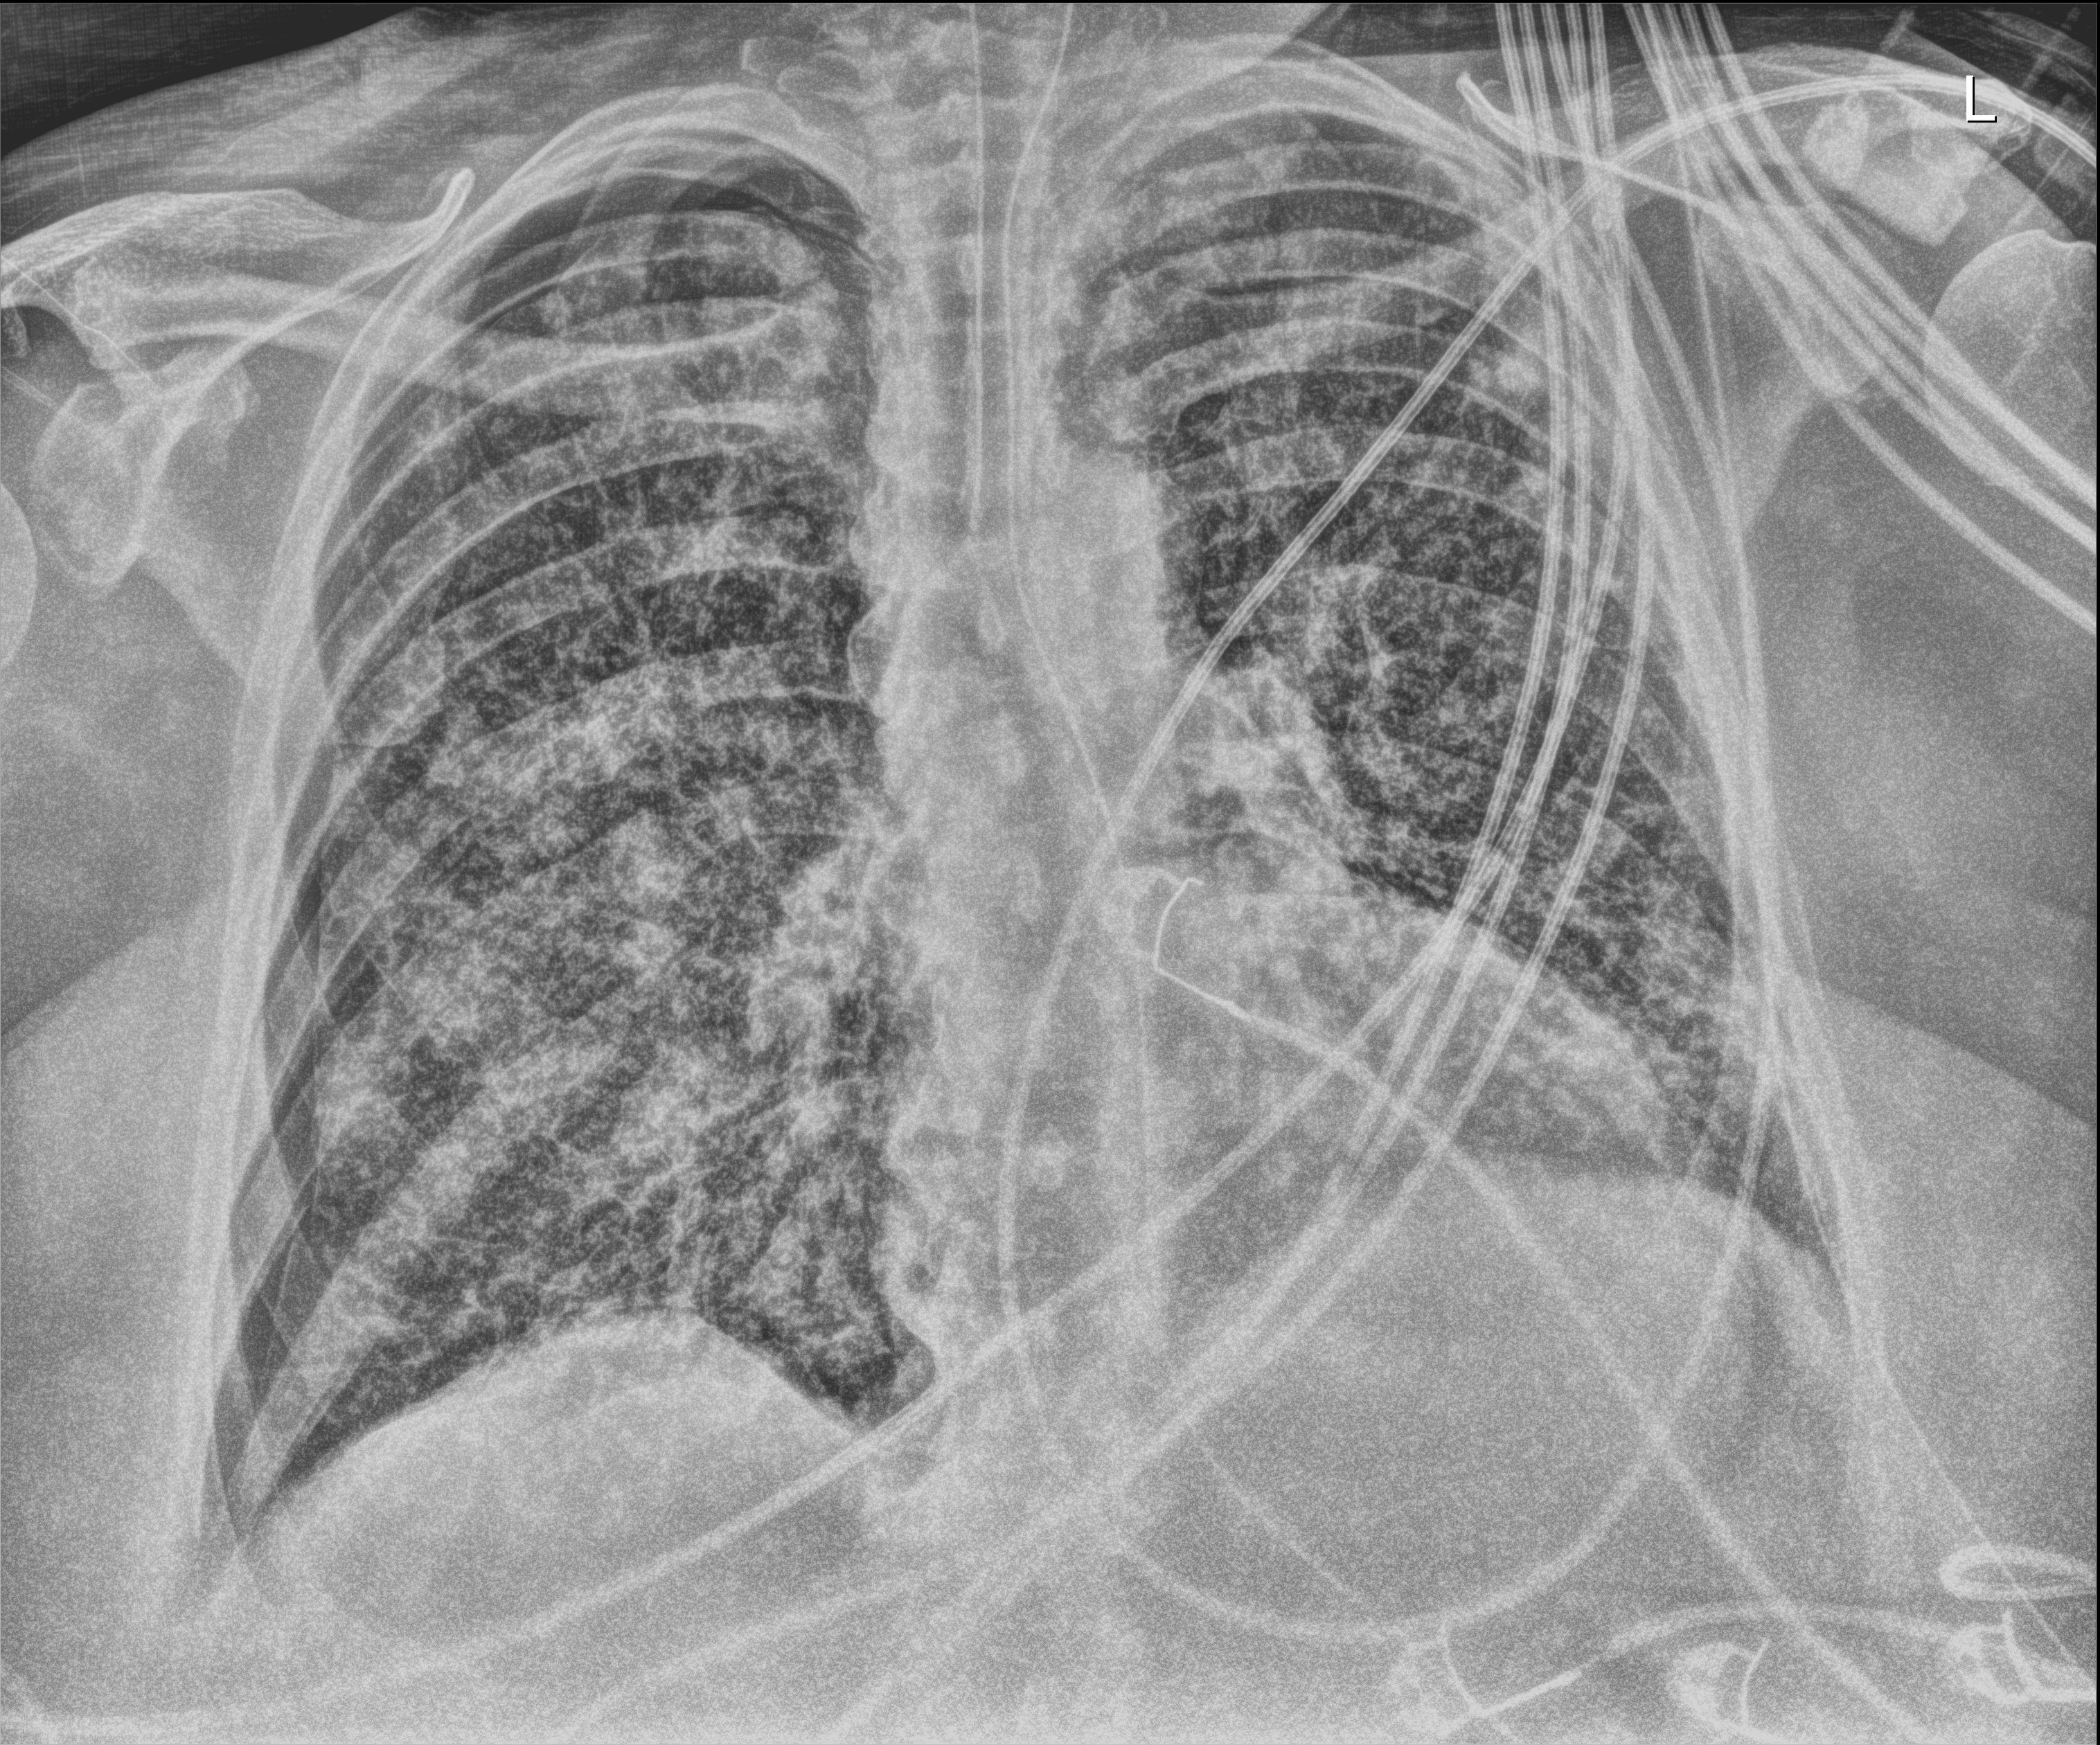
Portable chest radiograph; anteroposterior (AP) projection. Adult patient hospitalised with COVID-19, age 18–59 years.
Hospital-stay facts (about this admission, not read from this image; timing relative to this image not recorded): mechanically ventilated during this hospital stay: yes; admitted to intensive care during this hospital stay: yes.